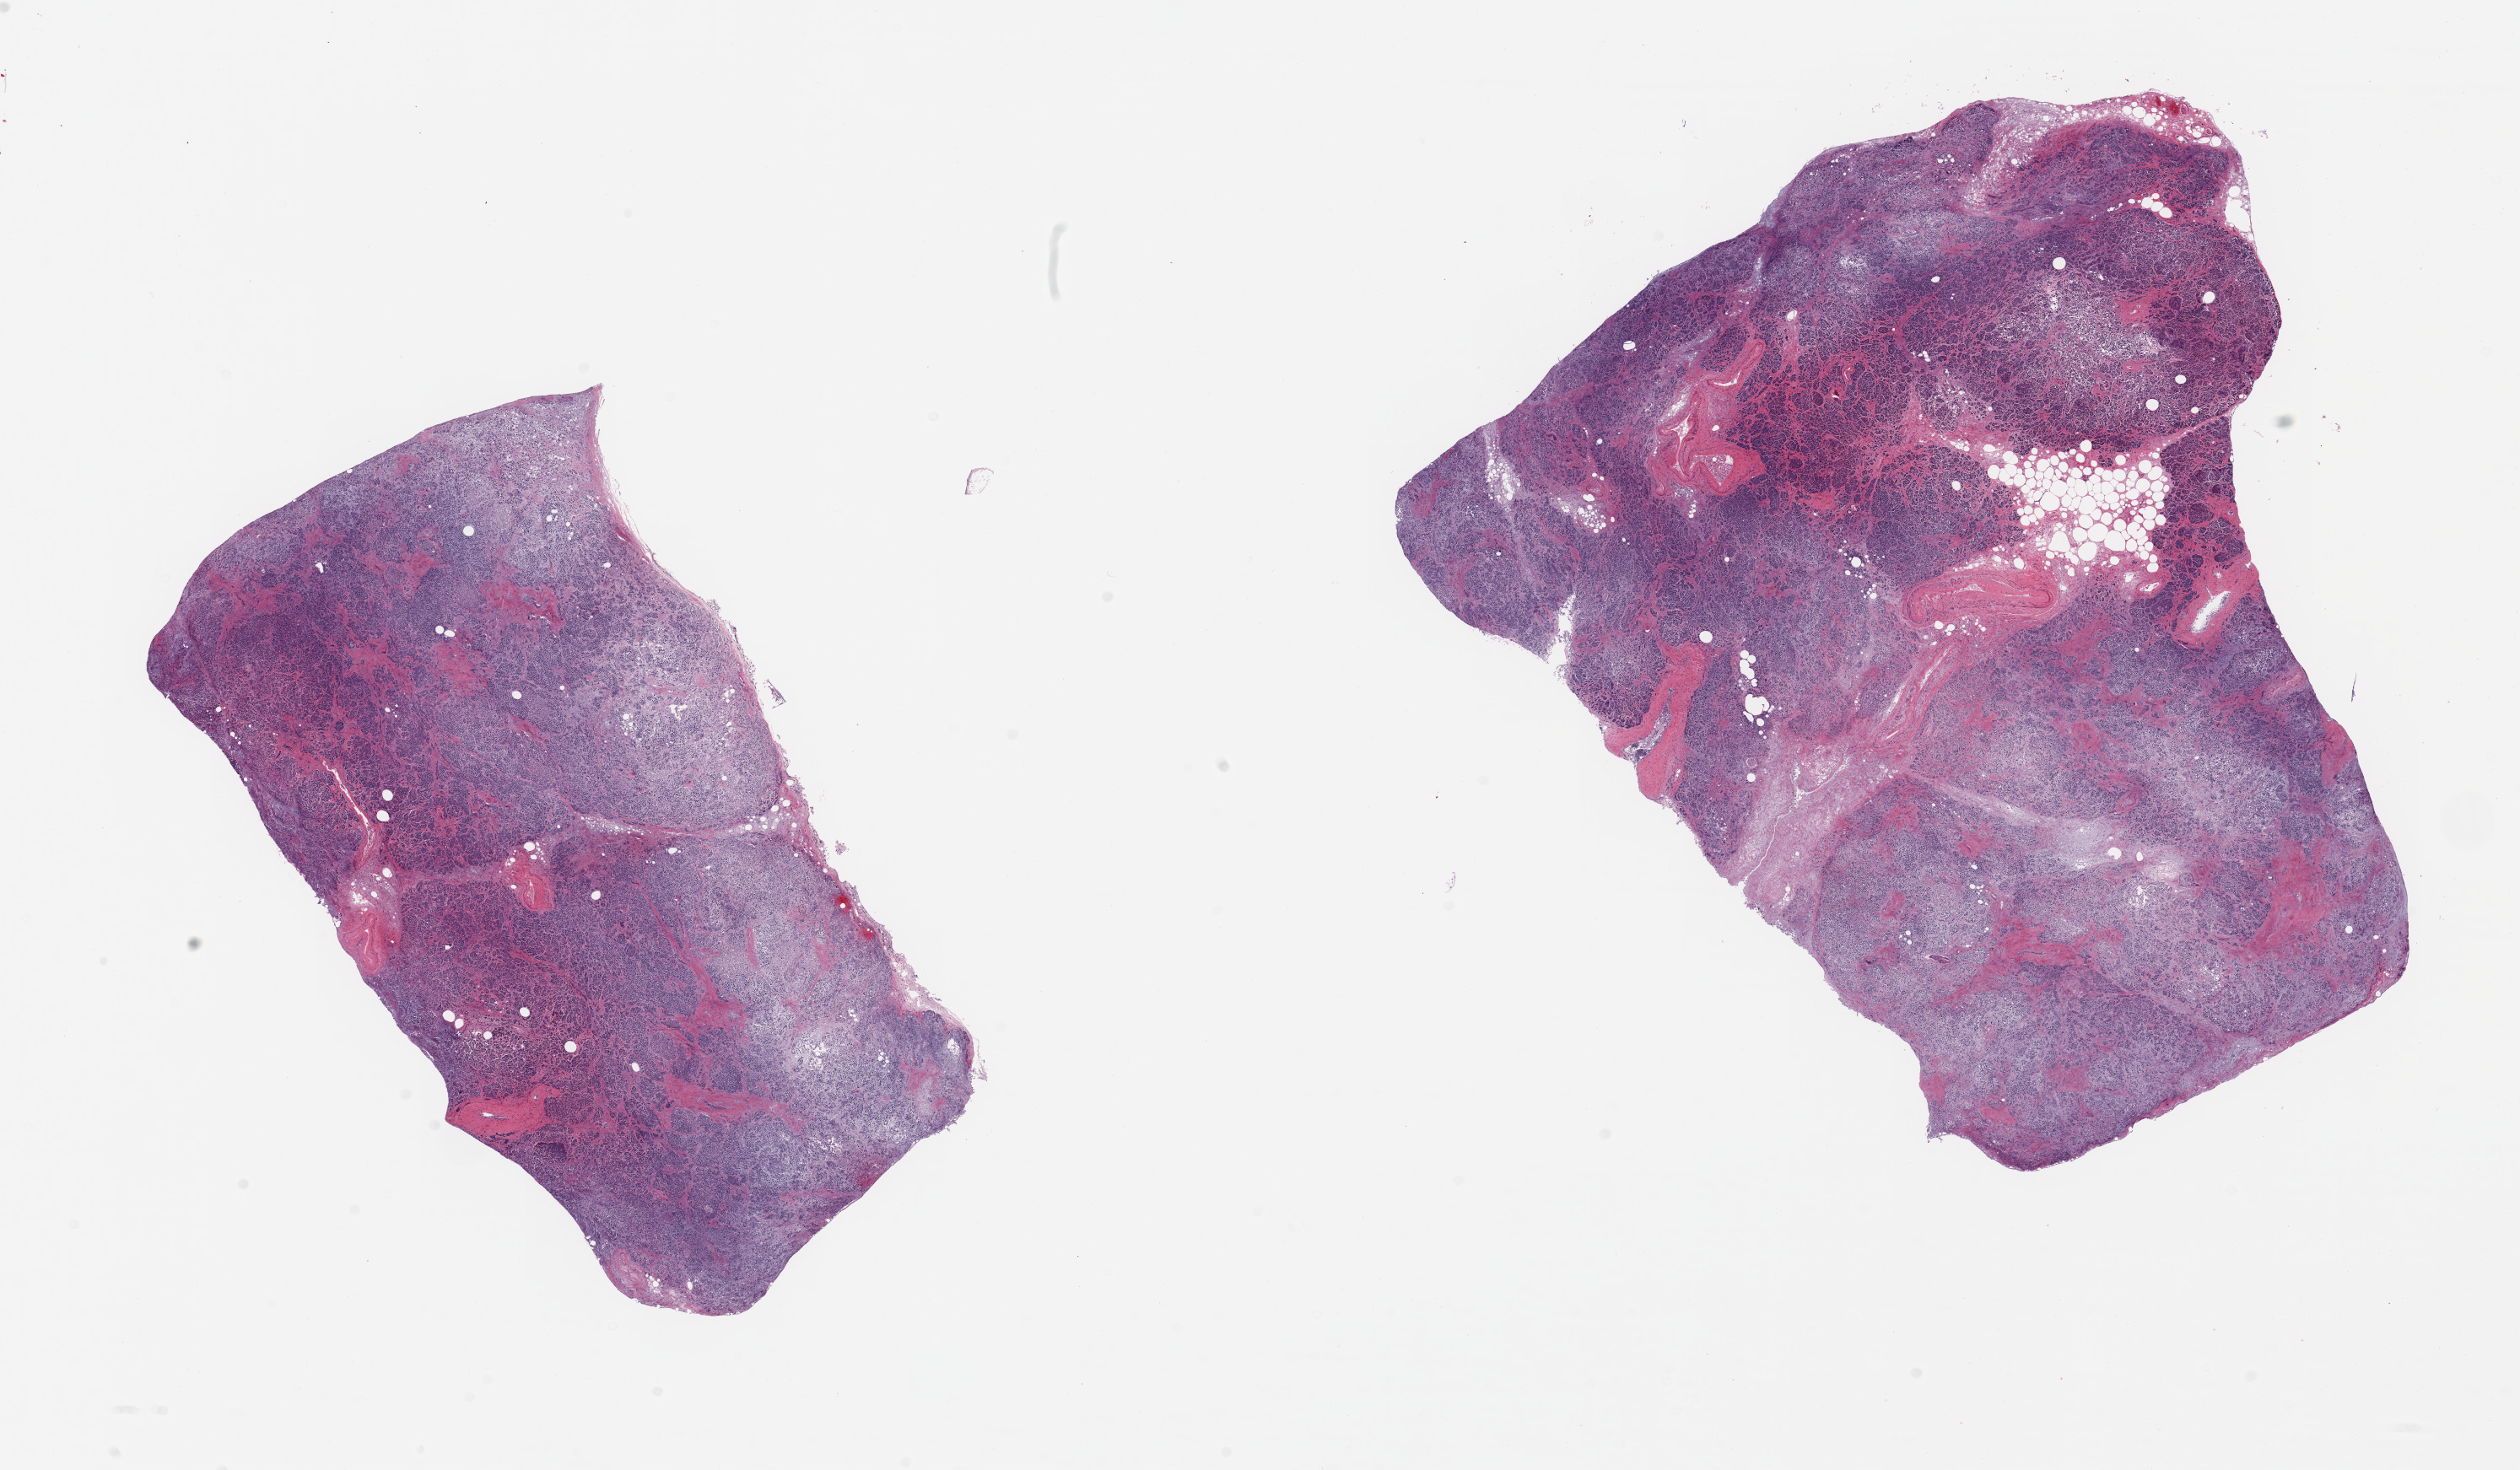
Hematoxylin and eosin (H&E) whole-slide image, low-resolution overview of the scanned area, about 23.6 x 13.8 mm; PAXgene-fixed paraffin-embedded (PFPE) section; sampled site (target tissue): pancreas; donor tissue sample.
Review note (as recorded): 2 pieces; a few foci of moderate autolysis, but overall severe; cannot distinguish islets from exocrine tissue.